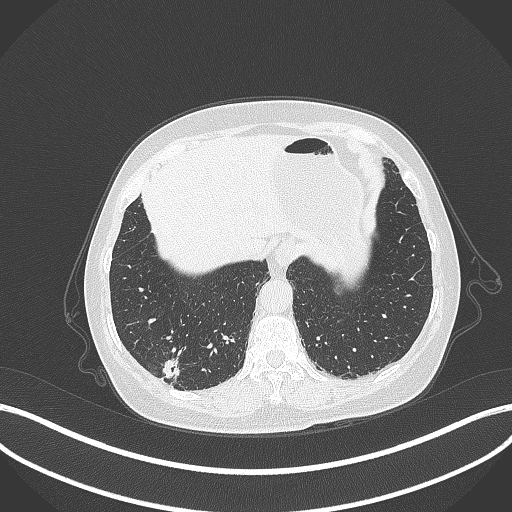
Chest CT, one axial slice. Position 53 of 333 along the scan axis. 120 kVp. Lung window (W 1500 / L -600 HU). 512 × 512 image matrix, field of view 400 × 400 mm. Patient: female, 69 years. From the clinical record (not read from this slice): clinical TNM (as recorded): T1b N0 M0; histopathological grade: G2-3.
Outlined on this slice (rectangle marked by the reading radiologist):
- lung tumour (recorded histology: adenocarcinoma): bounding box <161,357,182,383> (left, top, right, bottom; pixels)